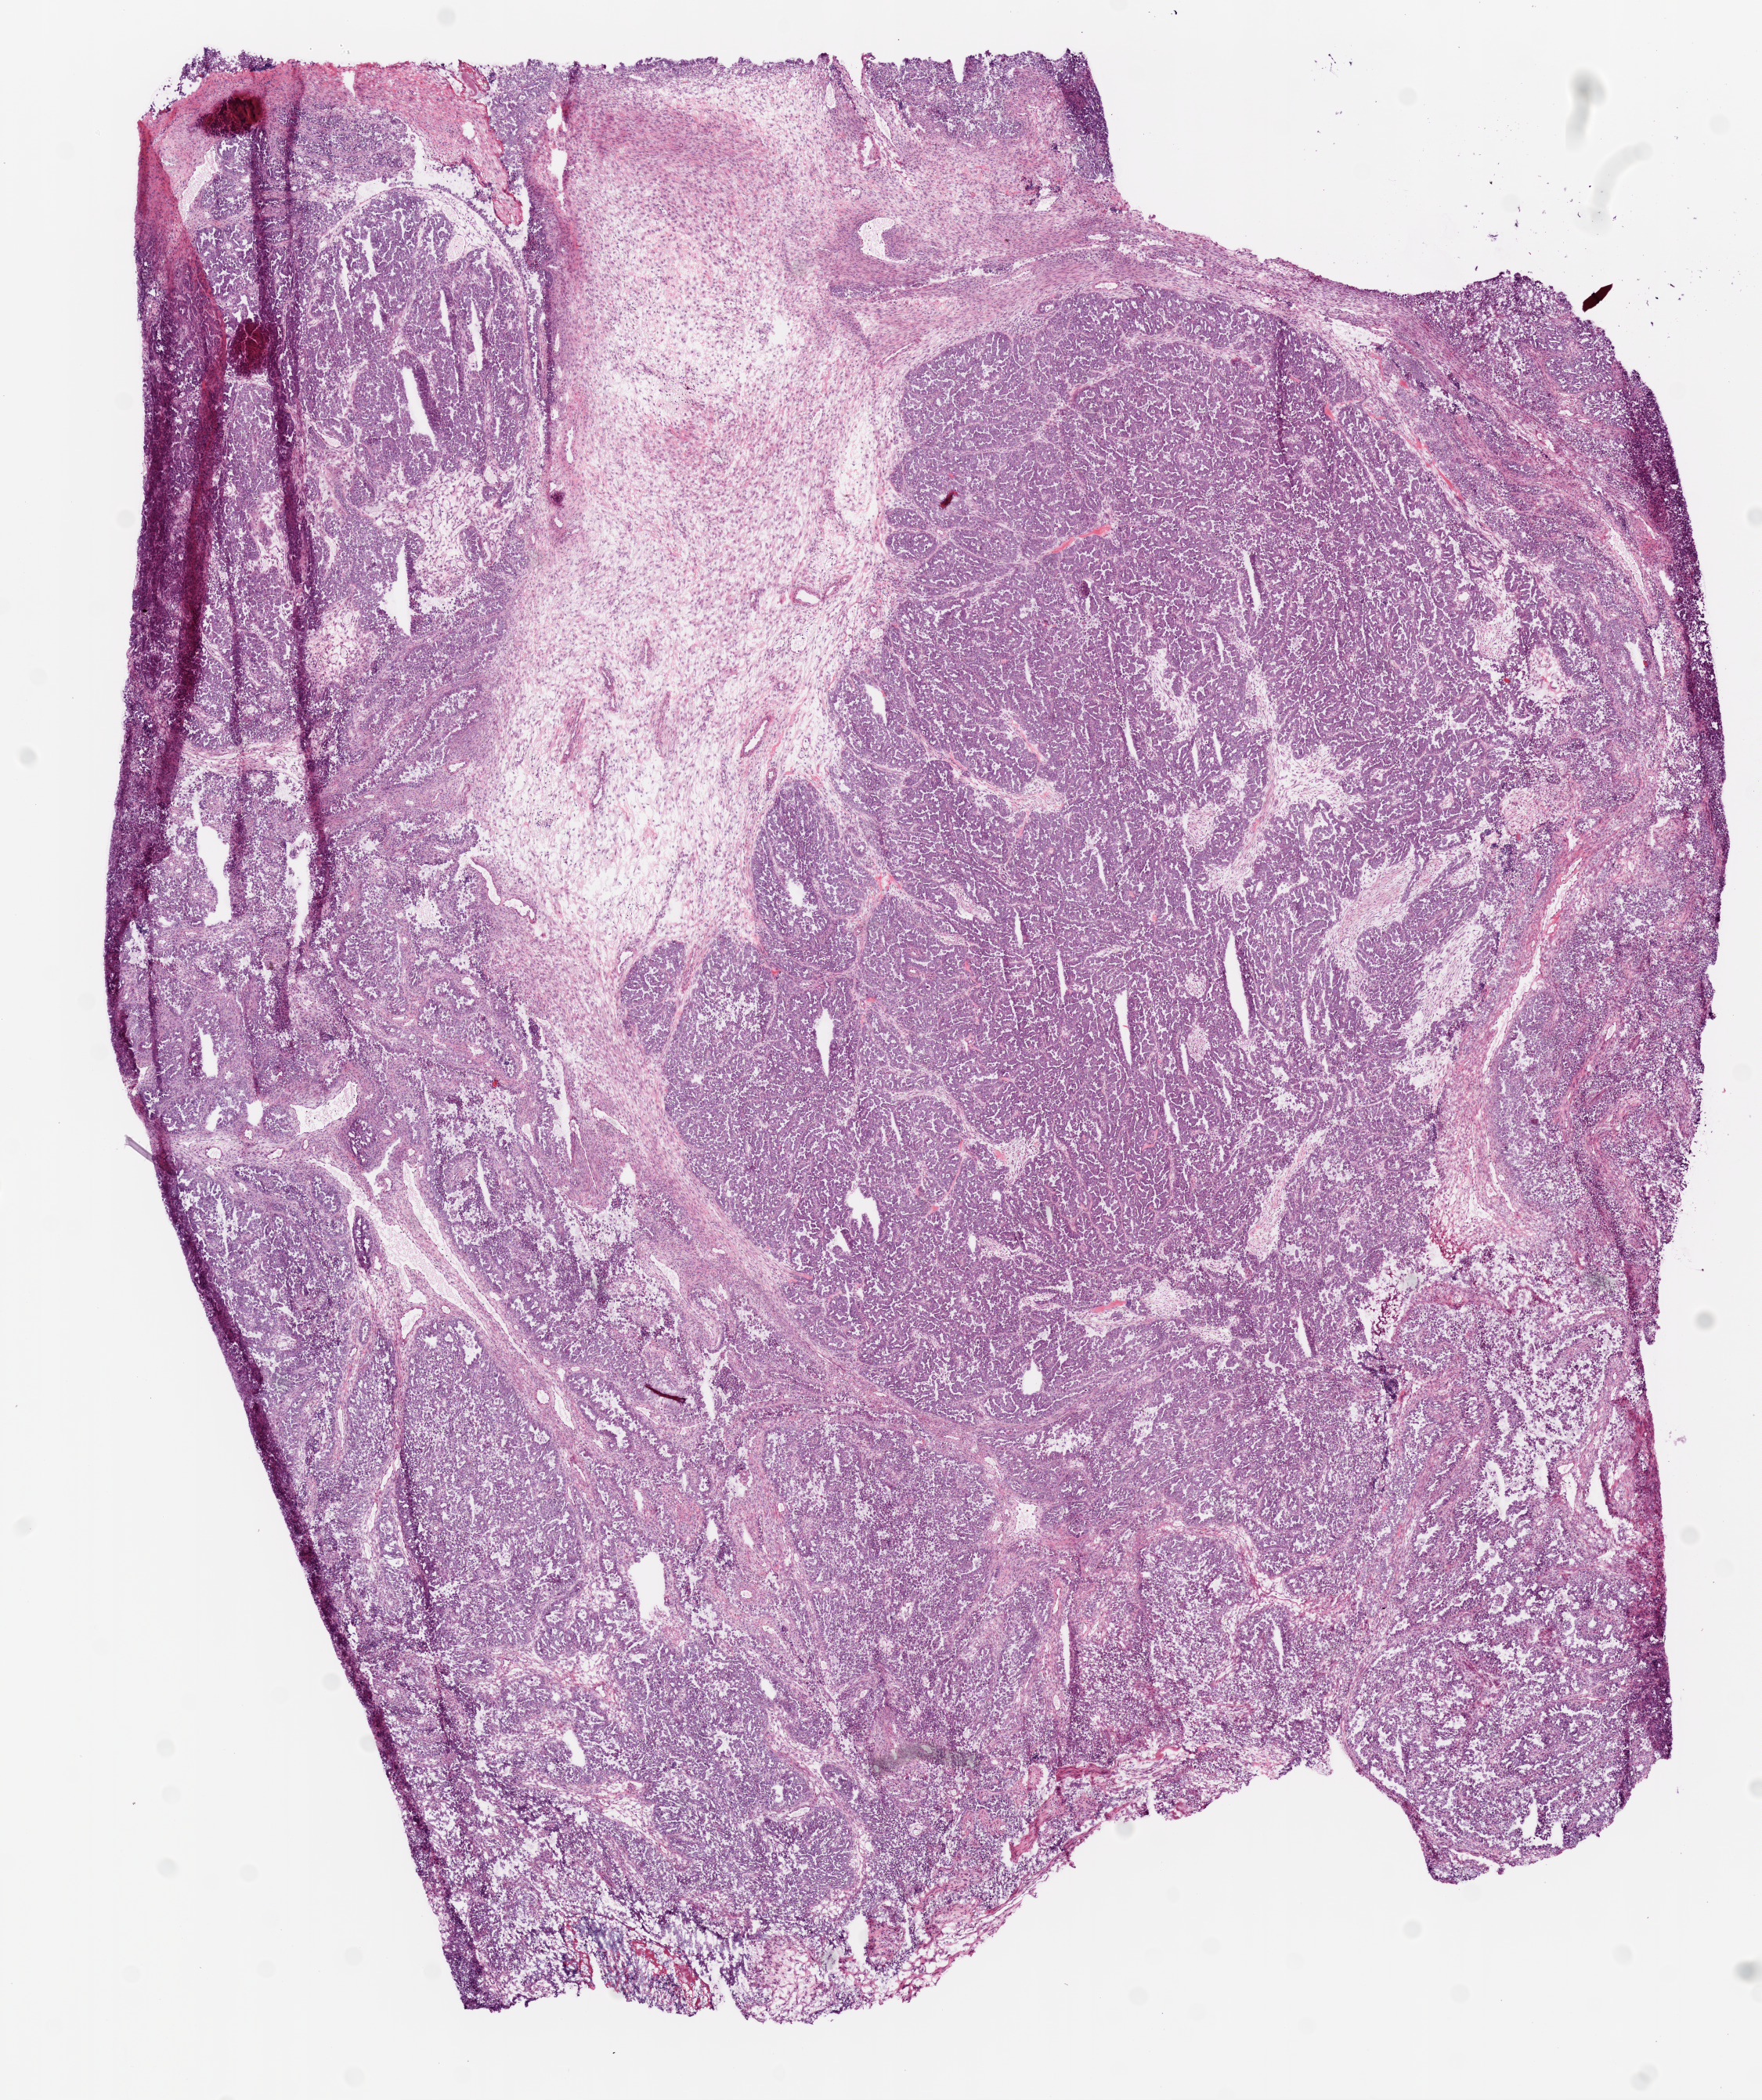
Whole-slide histology image, Hematoxylin and eosin (H&E) stained — shown as a low-resolution overview of the whole scanned area (about 9.0 x 10.8 mm, acquisition: 20x scan), frozen section from the bottom of the tissue portion, ovary, primary tumour sample. Female patient; age at initial diagnosis 71 years. Histologic grade: G3 (poorly differentiated). Slide review estimates, as recorded: tumour cells 88%, tumour nuclei 90%, normal cells 1%, stromal cells 10%, necrosis 1%.
• pathologic diagnosis: Serous cystadenocarcinoma, NOS
• FIGO stage: IIIC